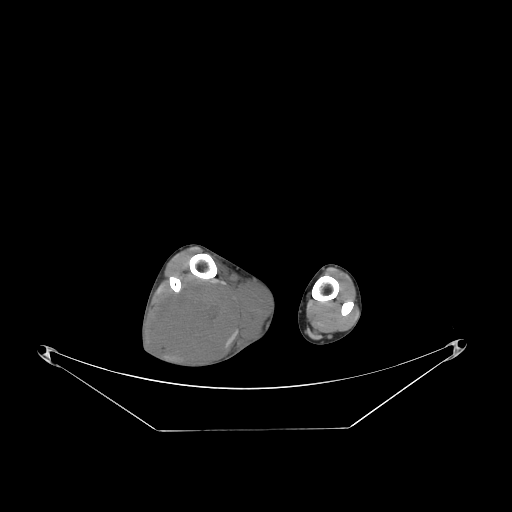
CT of an extremity soft-tissue mass (from a PET/CT study), one axial slice; slice 67 of 267 in the series (ordered by position); soft-tissue window (W 400 / L 40 HU); 3.75 mm slice thickness; 512 × 512 image matrix. Male patient. From the clinical record (not read from this slice): histological type: liposarcoma - round cell; grade: high; site of the primary tumour: right calf.
Outlined on this slice (expert contour drawn on MRI and transferred to this co-registered scan by the dataset authors):
- gross tumour volume (mass): box from (x=149, y=274) to (x=275, y=369) px